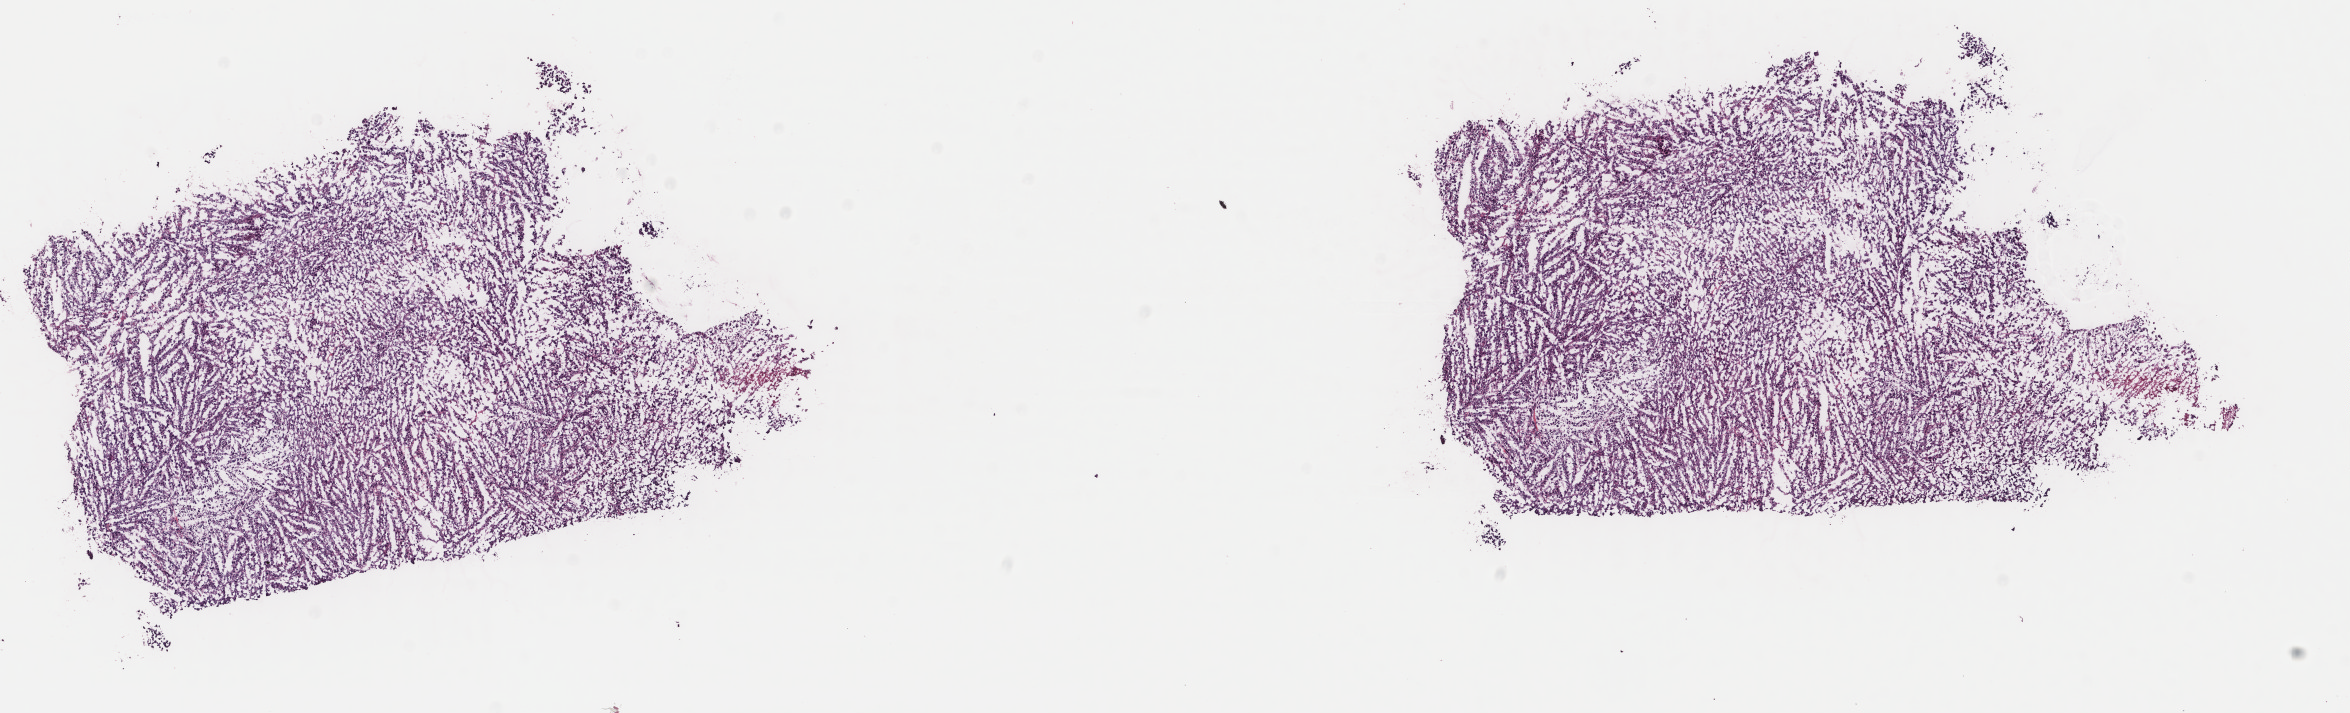
Whole-slide histology image, H&E-stained — a low-resolution overview of the entire scanned area, about 18.7 x 5.7 mm (from a 40x scan); frozen section from the top of the tissue portion; metastatic tumour sample, sampled site not recorded. Male, age 49 years at initial diagnosis. Composition of this section per pathologist review: tumour cells 100%, tumour nuclei 90%, normal cells 0%, stromal cells 0%, necrosis 0%. Inflammatory infiltration, as recorded: lymphocyte infiltration 0%, monocyte infiltration 0%, neutrophil infiltration 0%.
This section: metastatic tumour tissue. Patient diagnosis: Malignant melanoma, NOS.